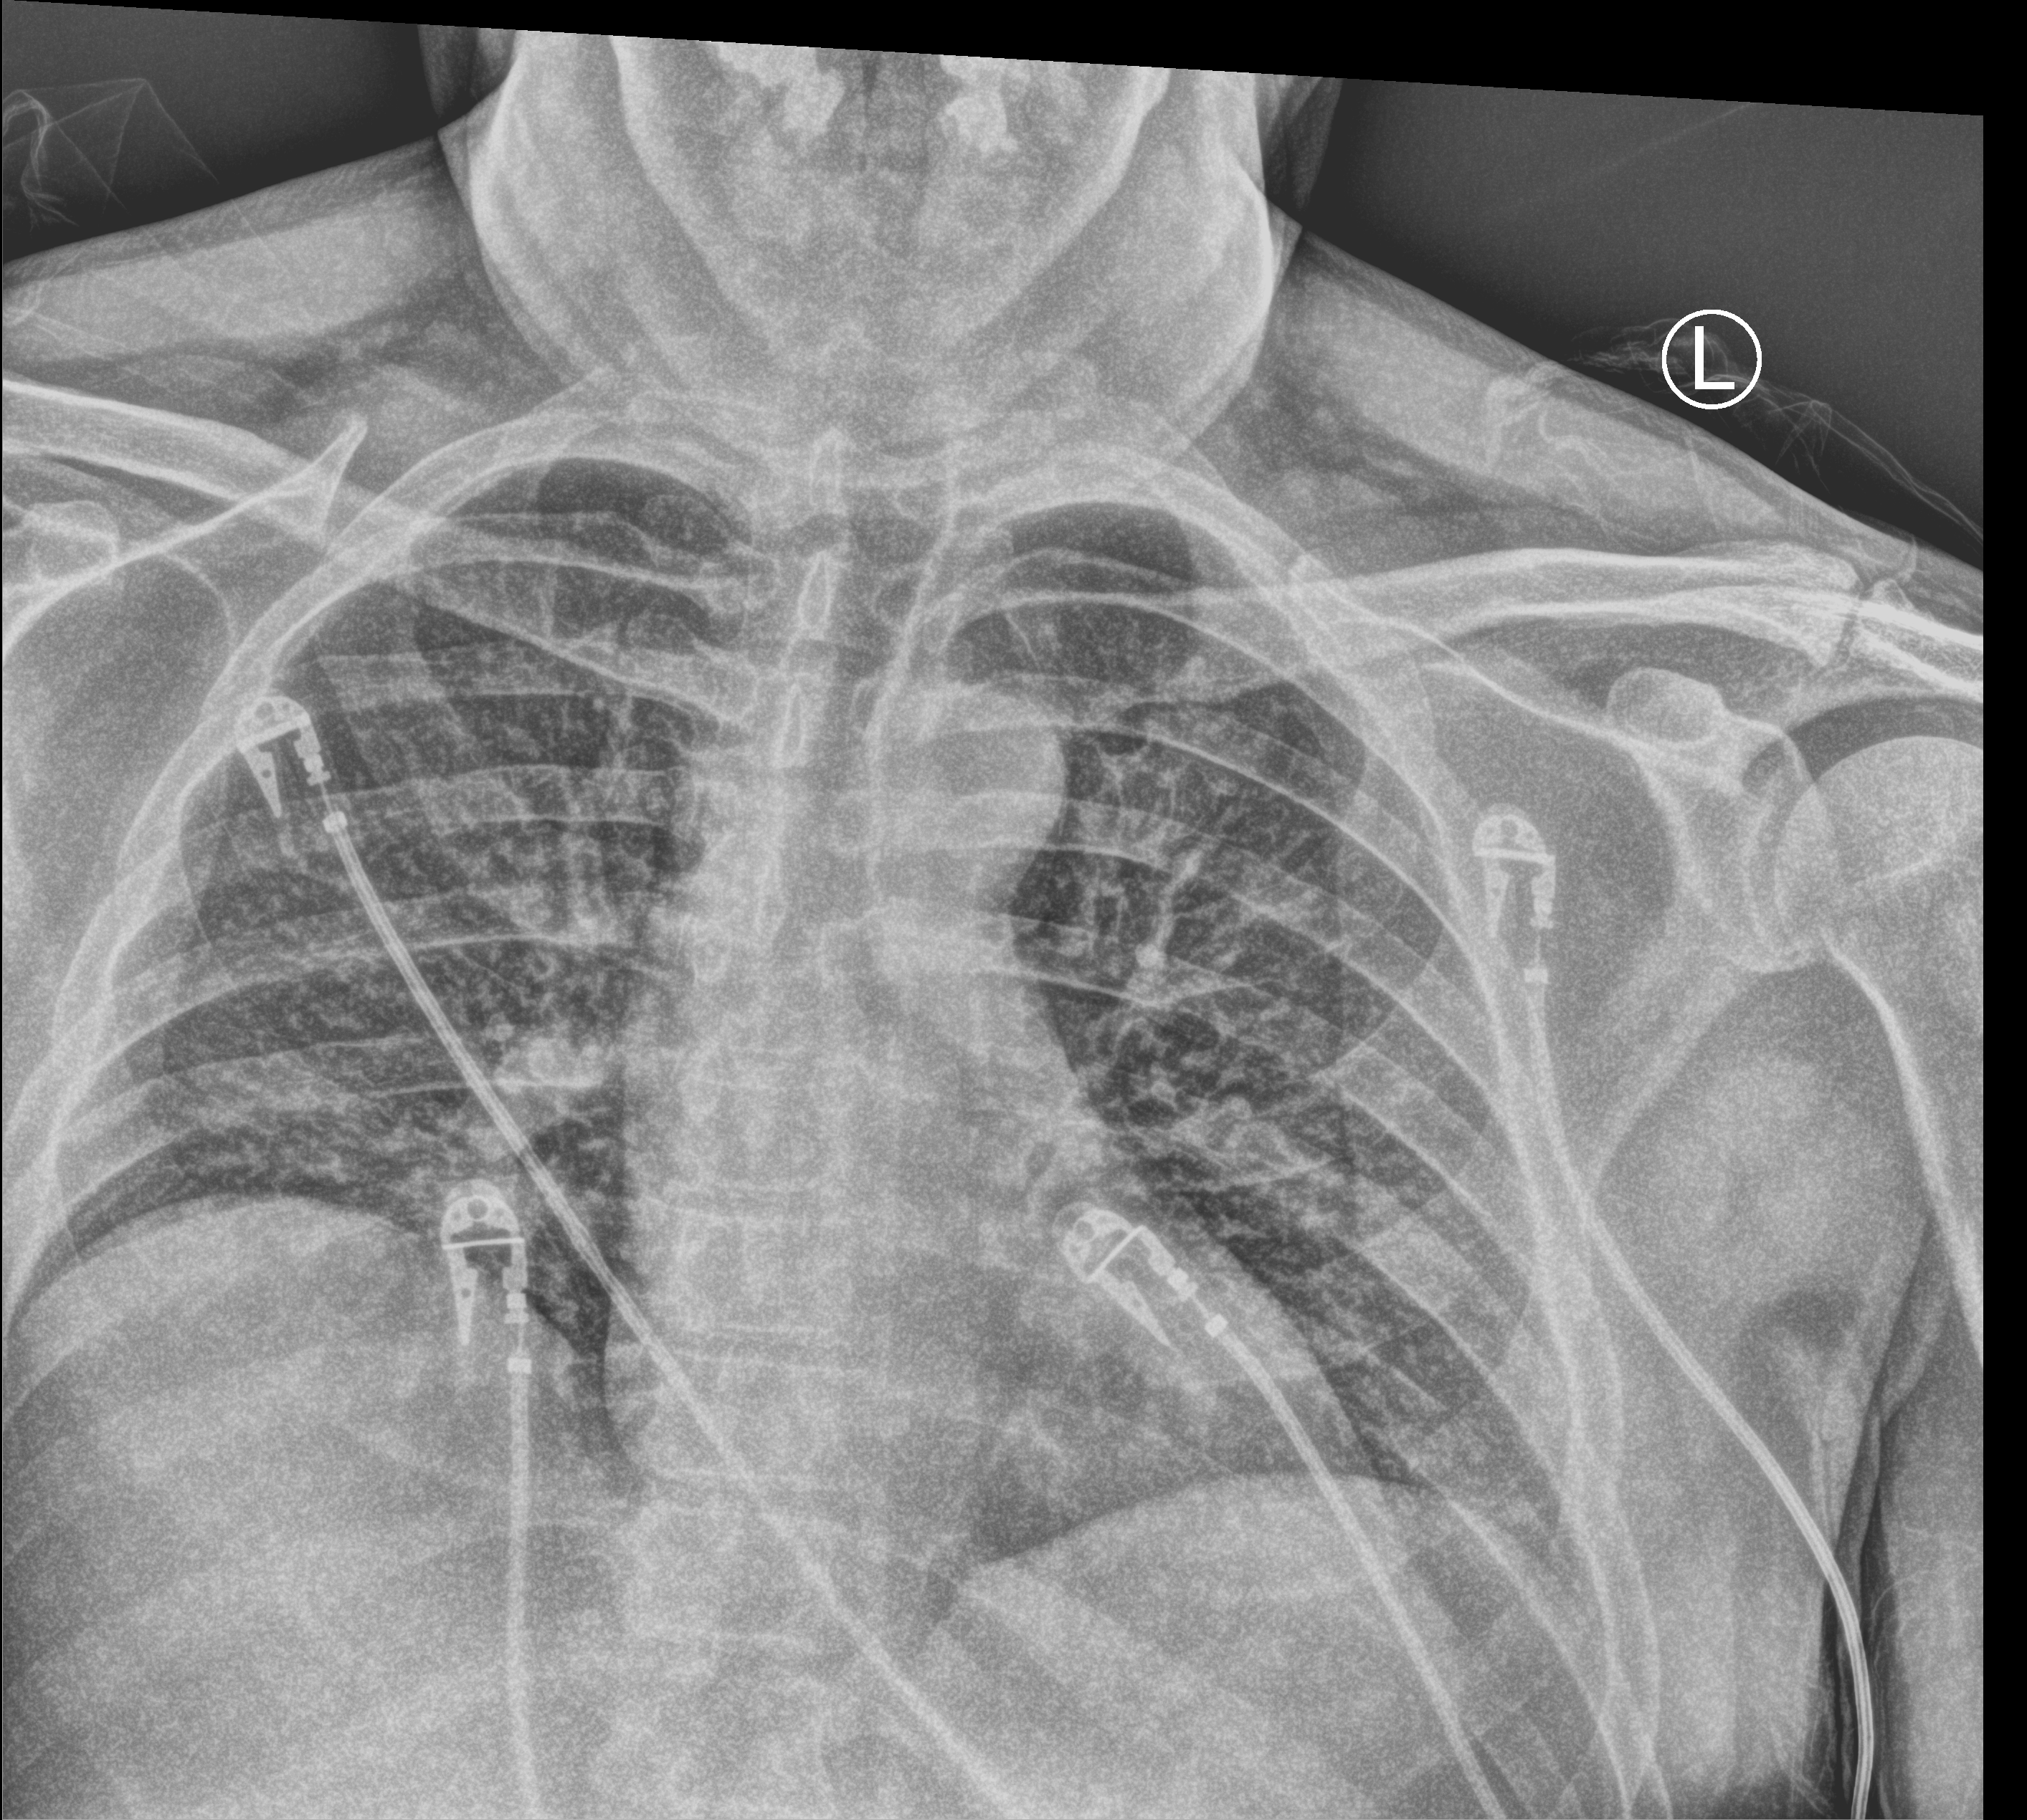
Portable chest radiograph. Patient hospitalised with COVID-19; male, aged 18–59 years.
Hospital-stay facts (about this admission, not read from this image; timing relative to this image not recorded): admitted to intensive care during this hospital stay: no; mechanically ventilated during this hospital stay: no.